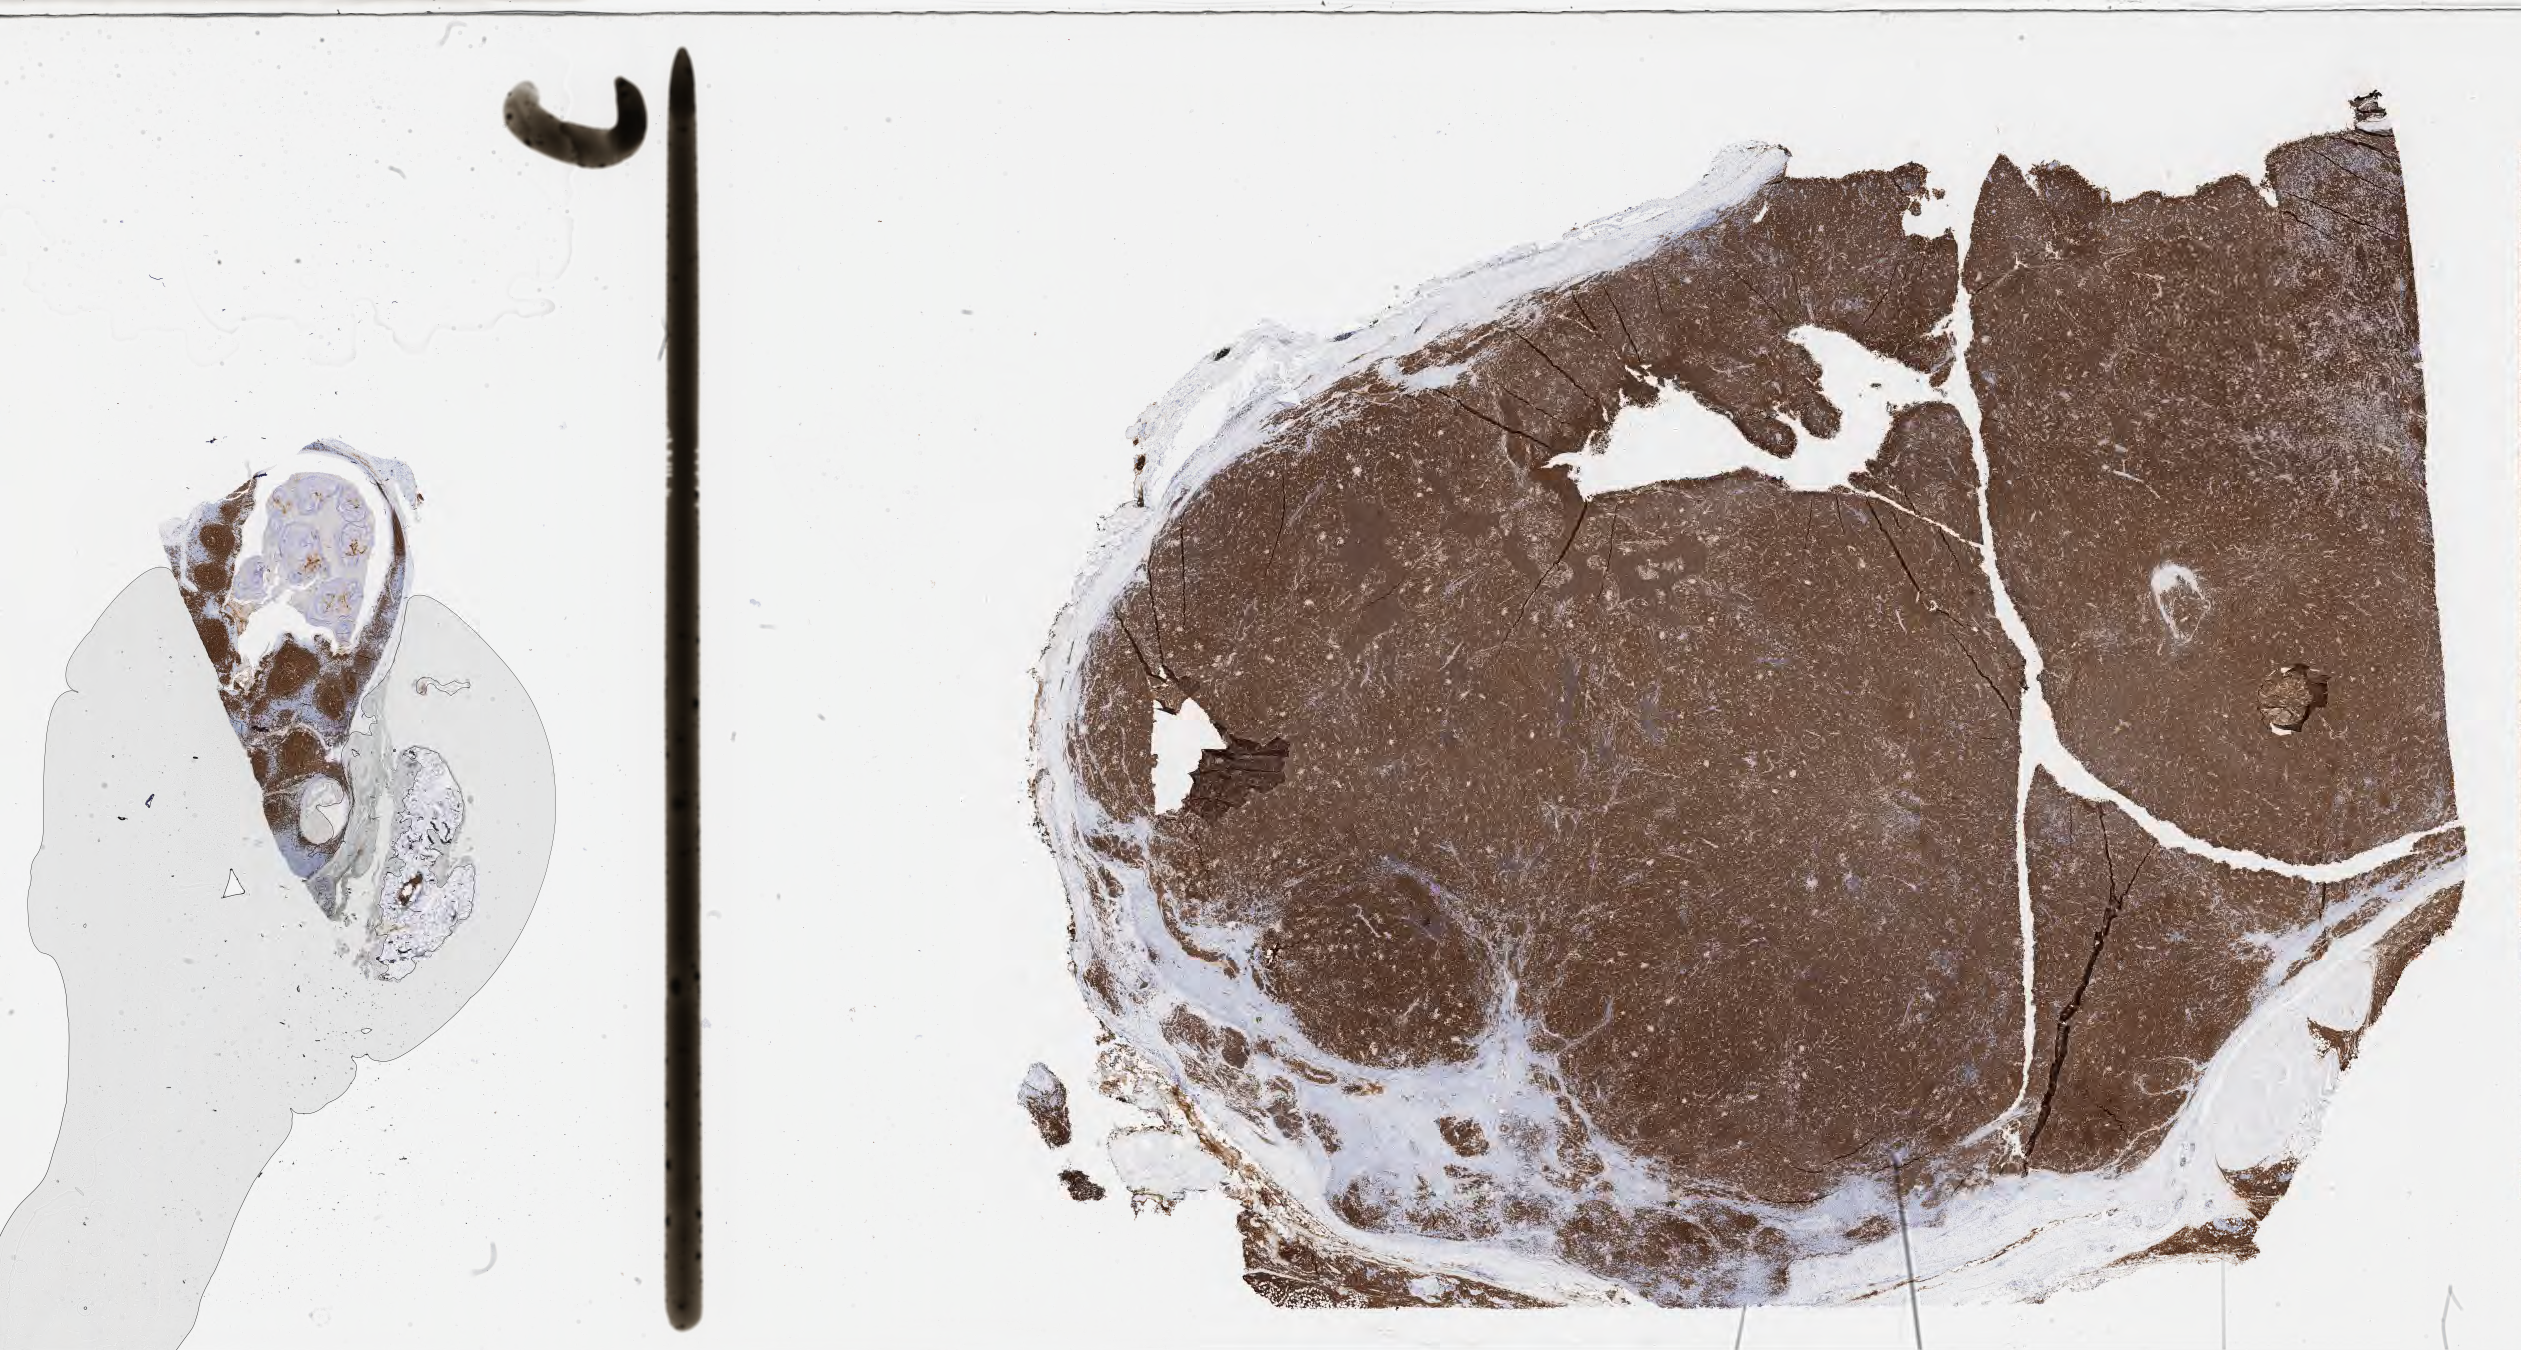
Immunohistochemistry (IHC) whole-slide image stained for CD20, a low-resolution overview of the entire scanned area, about 40.8 x 21.8 mm, specimen: tumor tissue. Patient male; aged 30.
* histologic diagnosis: Burkitt lymphoma, NOS